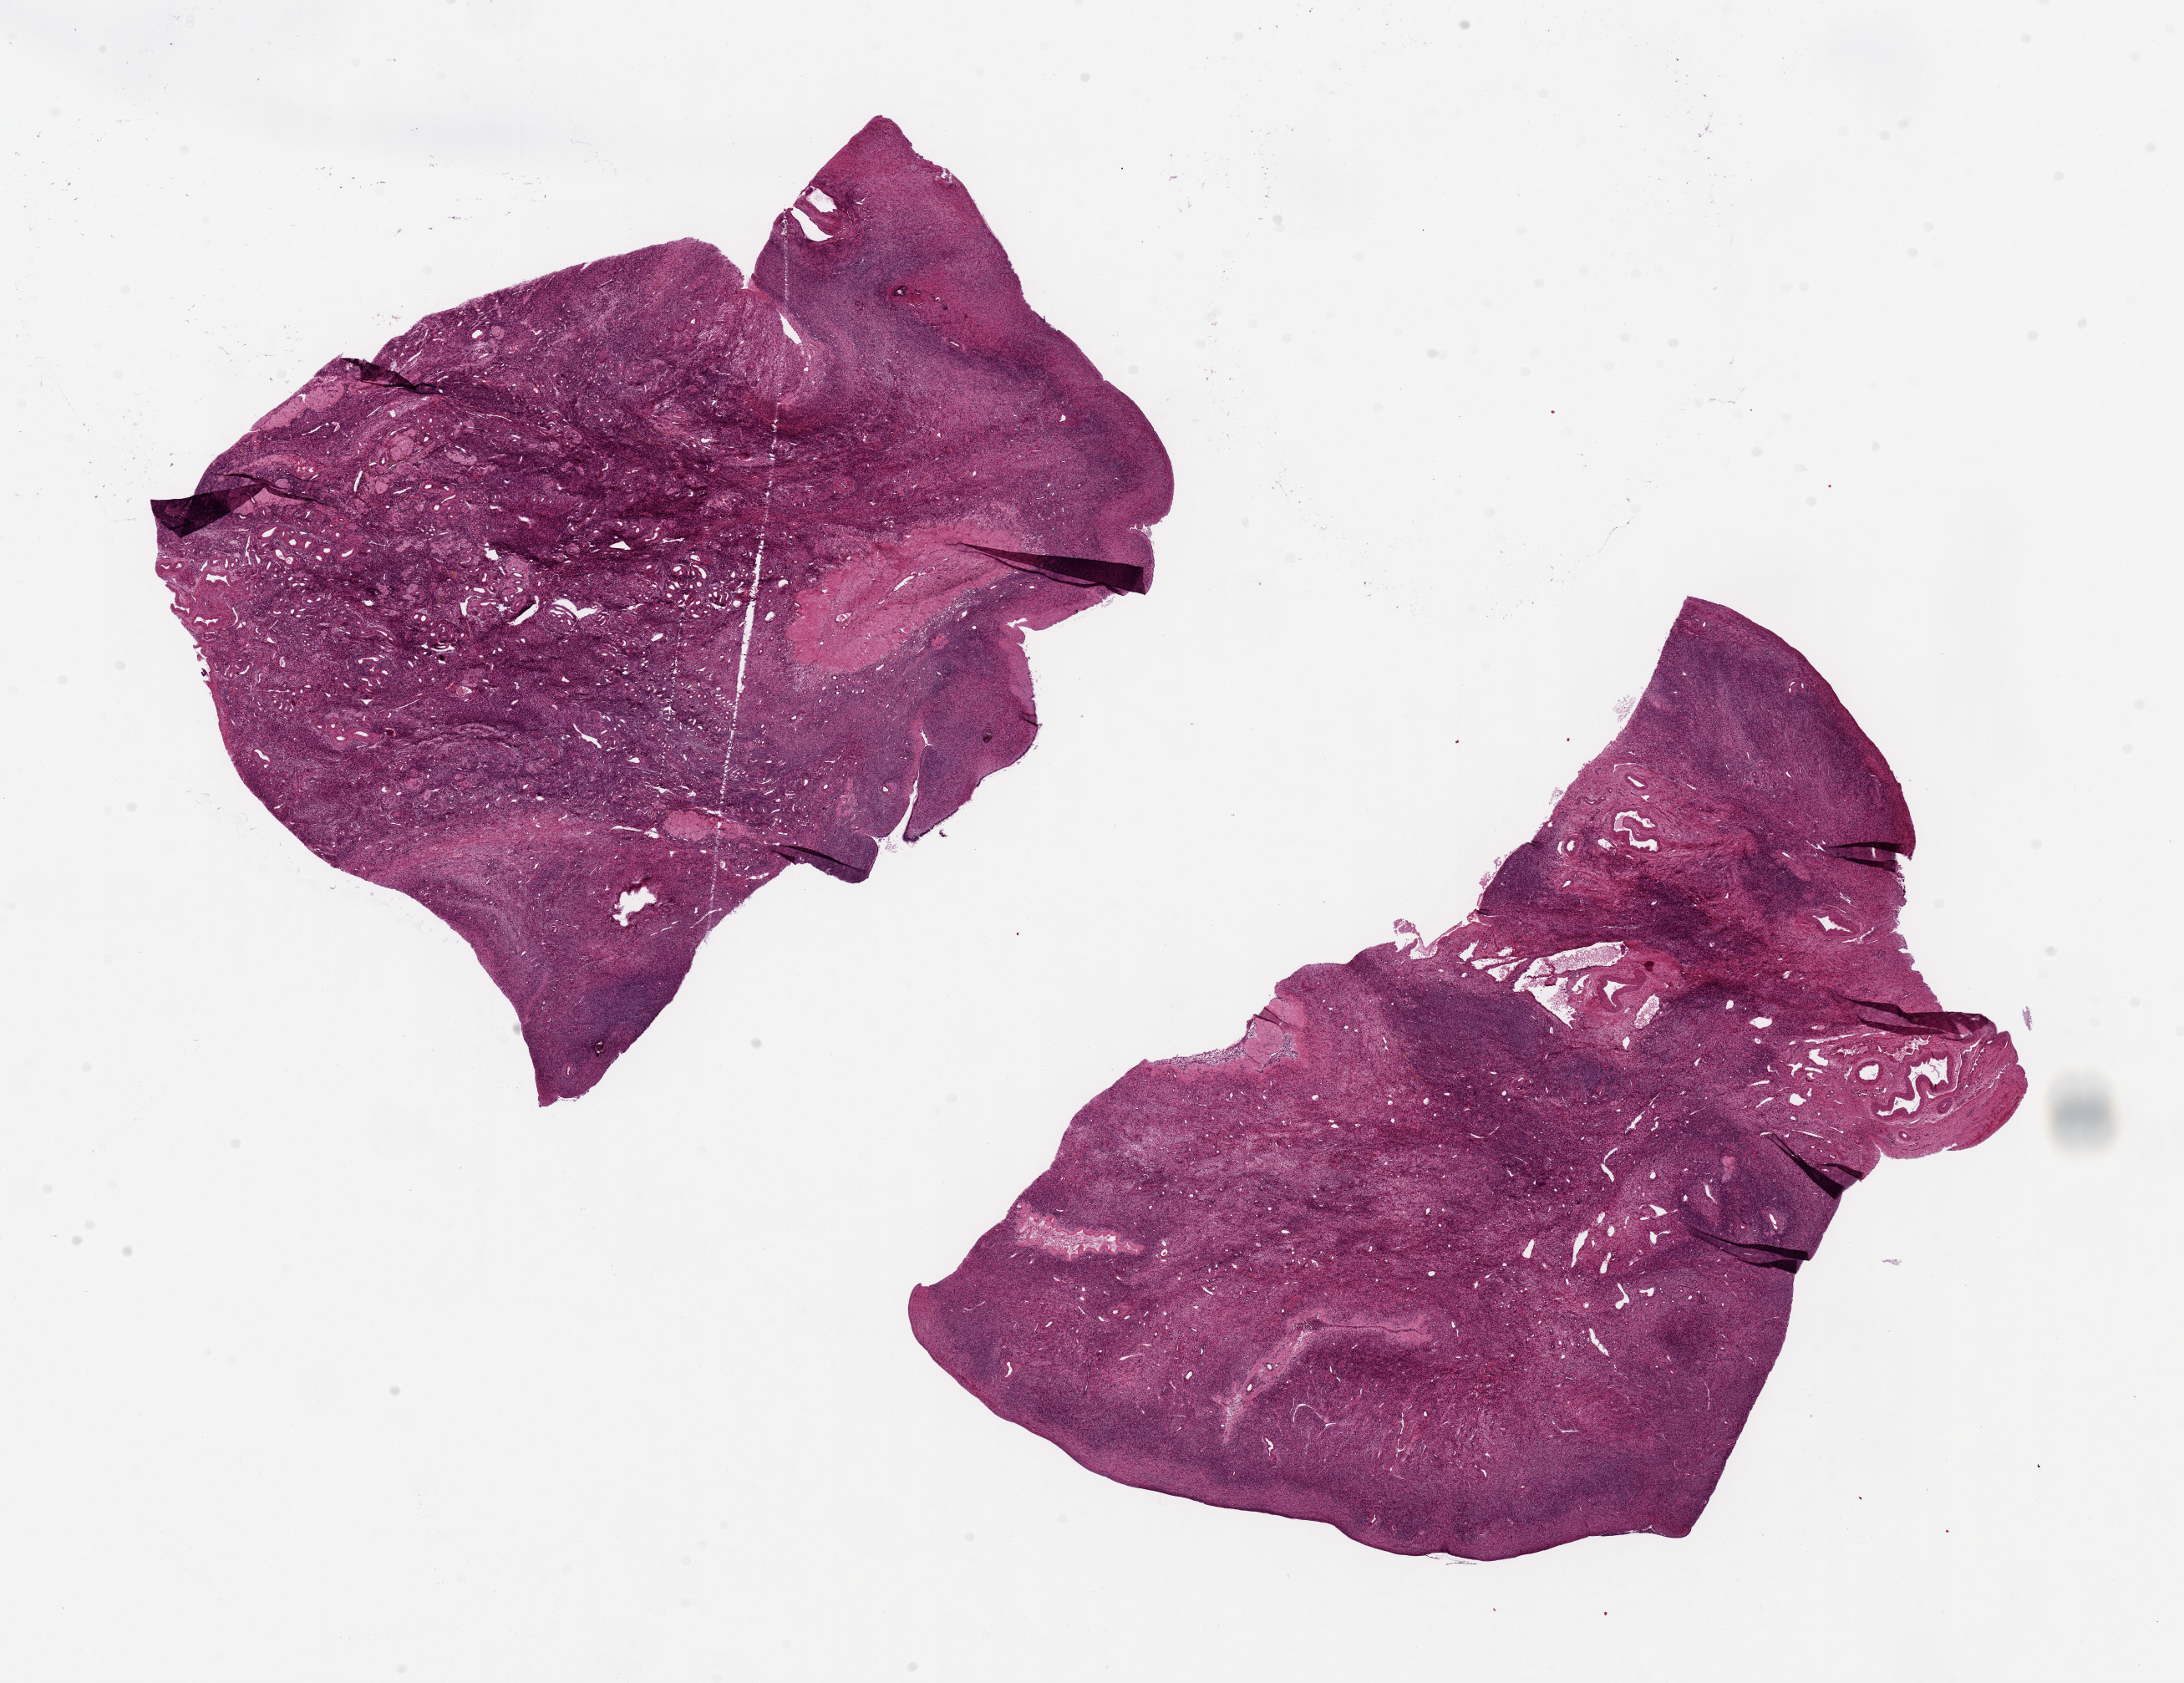
Whole-slide image, haematoxylin and eosin stain, low-resolution overview of the scanned area, about 20.7 x 15.9 mm (slide scanned at 20x). PAXgene-fixed, paraffin-embedded tissue. Sampled site (target tissue): ovary. Tissue donor sample. Donor: female.
- review note (as recorded): 2 pieces, 10x7 & 8x7 mm; ova seen; peritoneal surface present